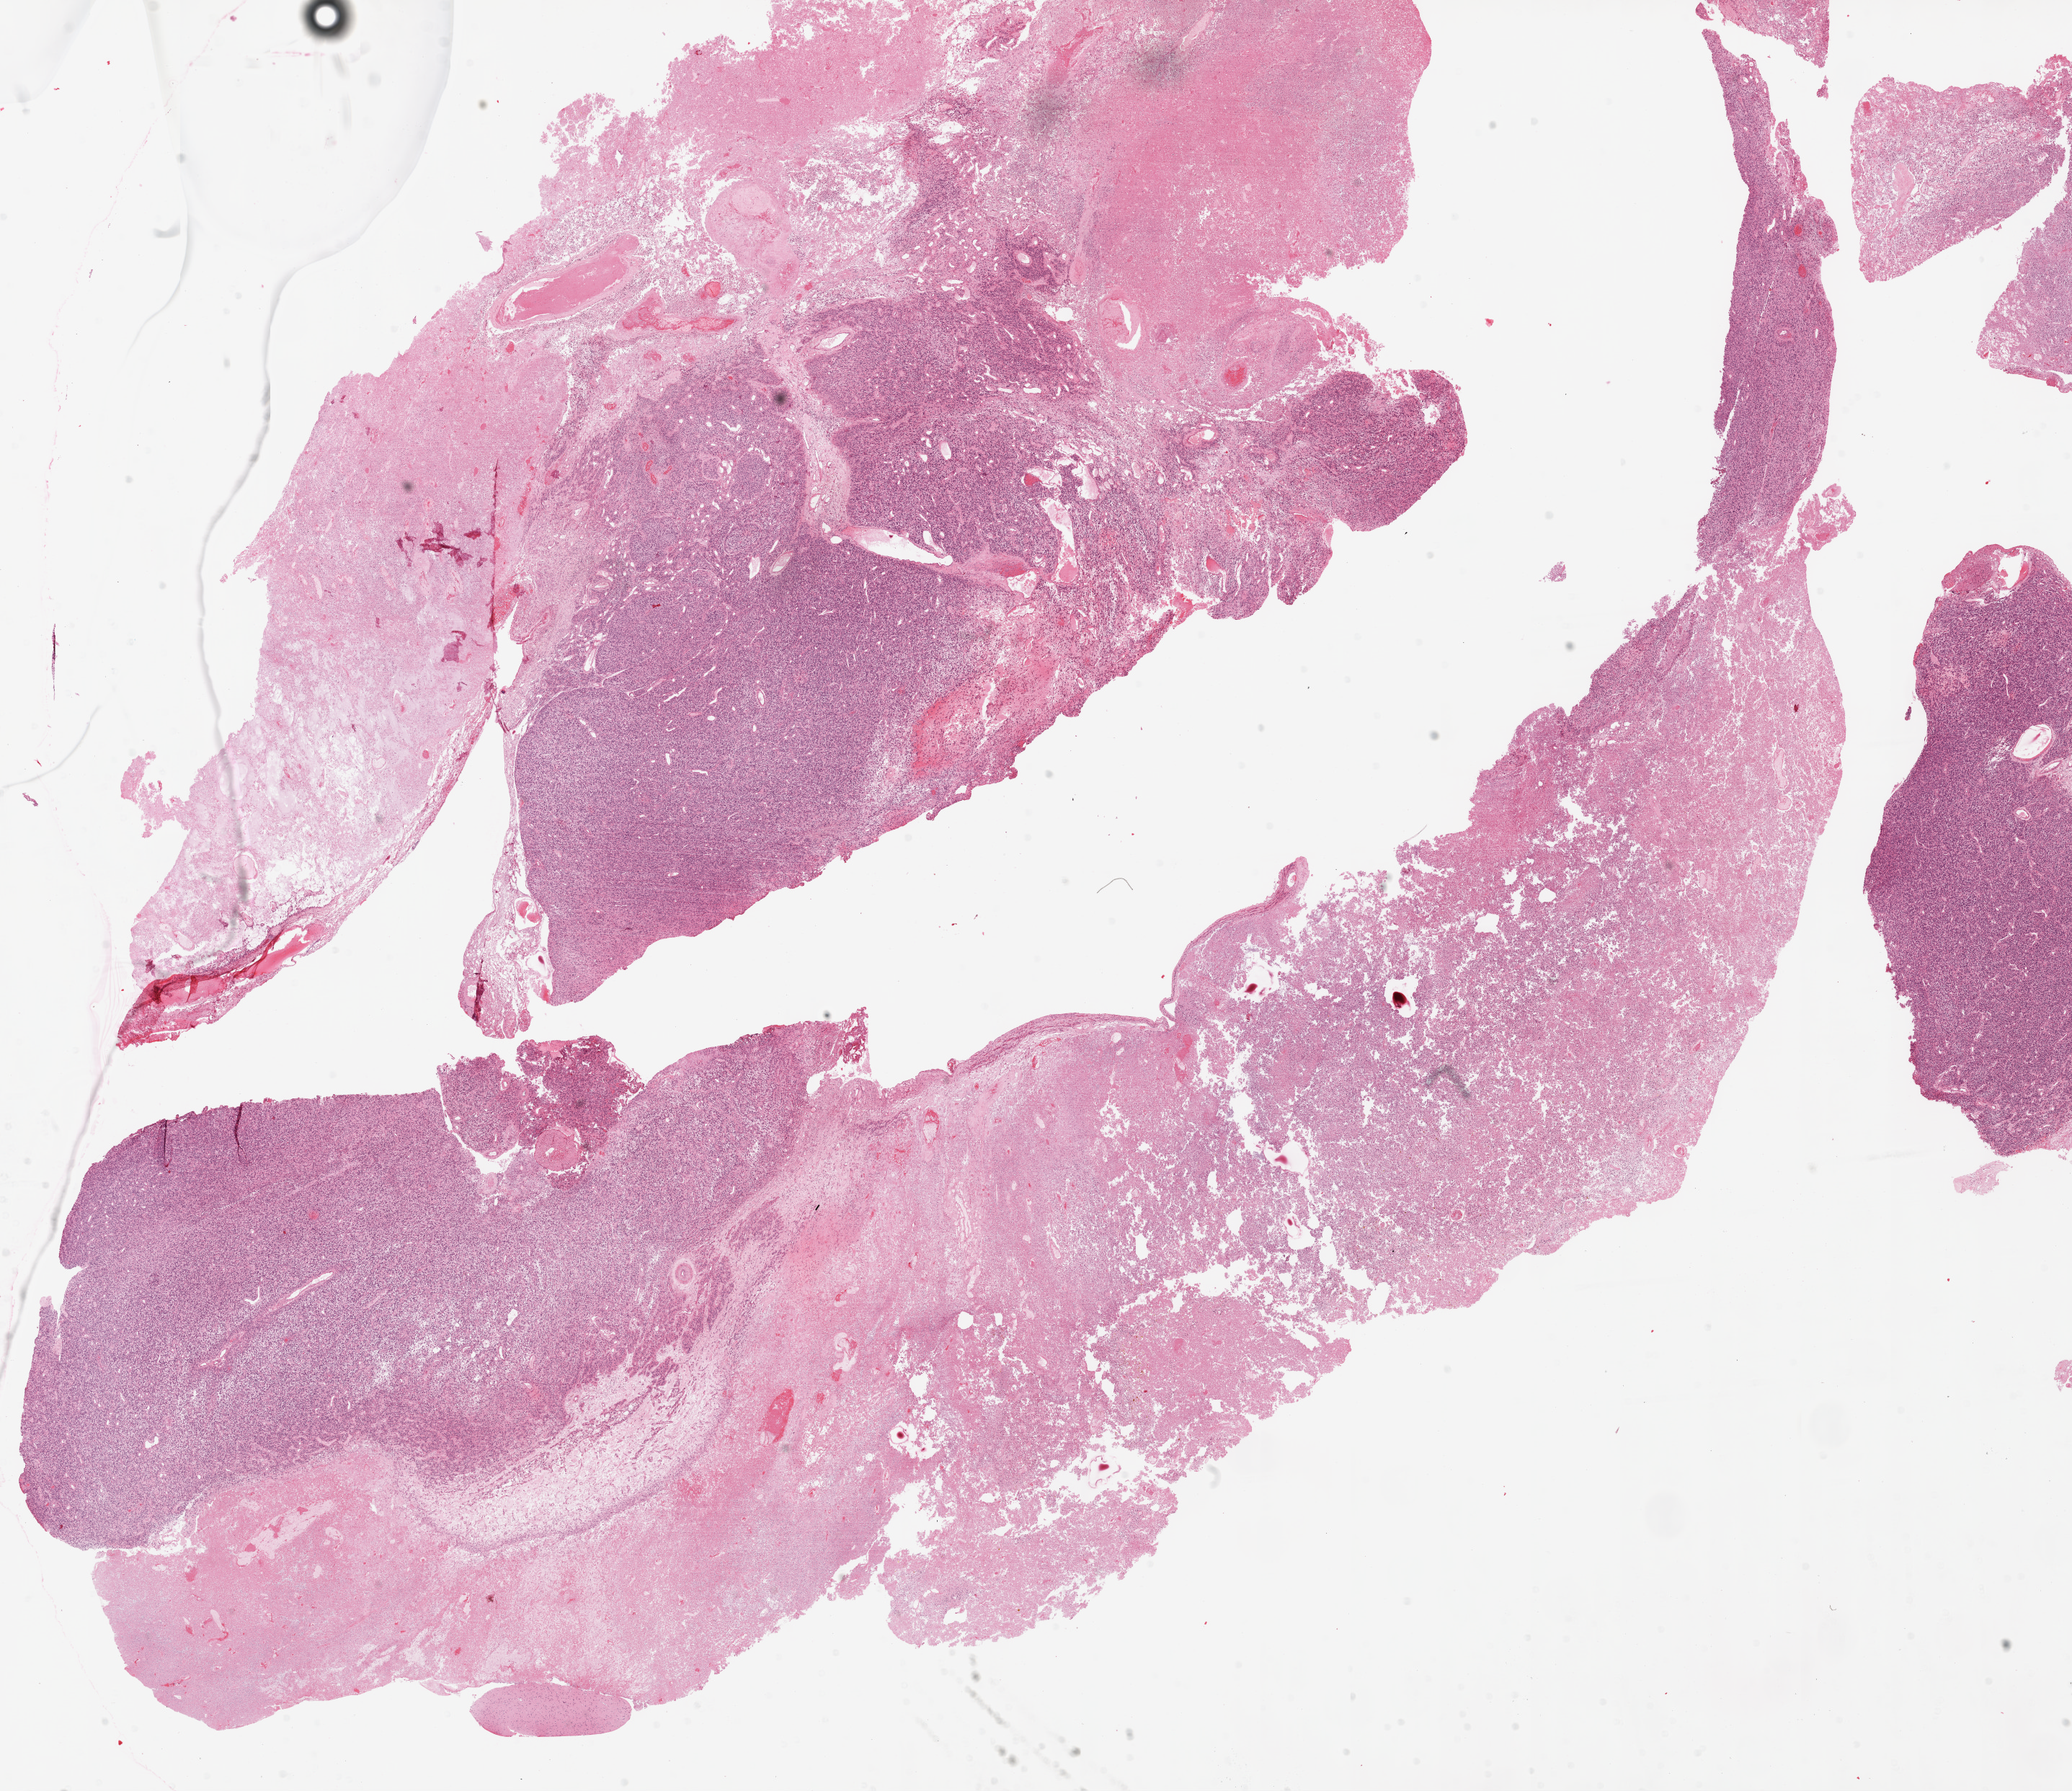
Digitized H&E tissue section (whole slide) — shown as a low-resolution overview of the whole scanned area (about 23.1 x 19.9 mm, from a 20x scan); FFPE section; brain, primary tumour sample. Female, age 67 years at initial diagnosis.
Pathologic diagnosis: Glioblastoma.